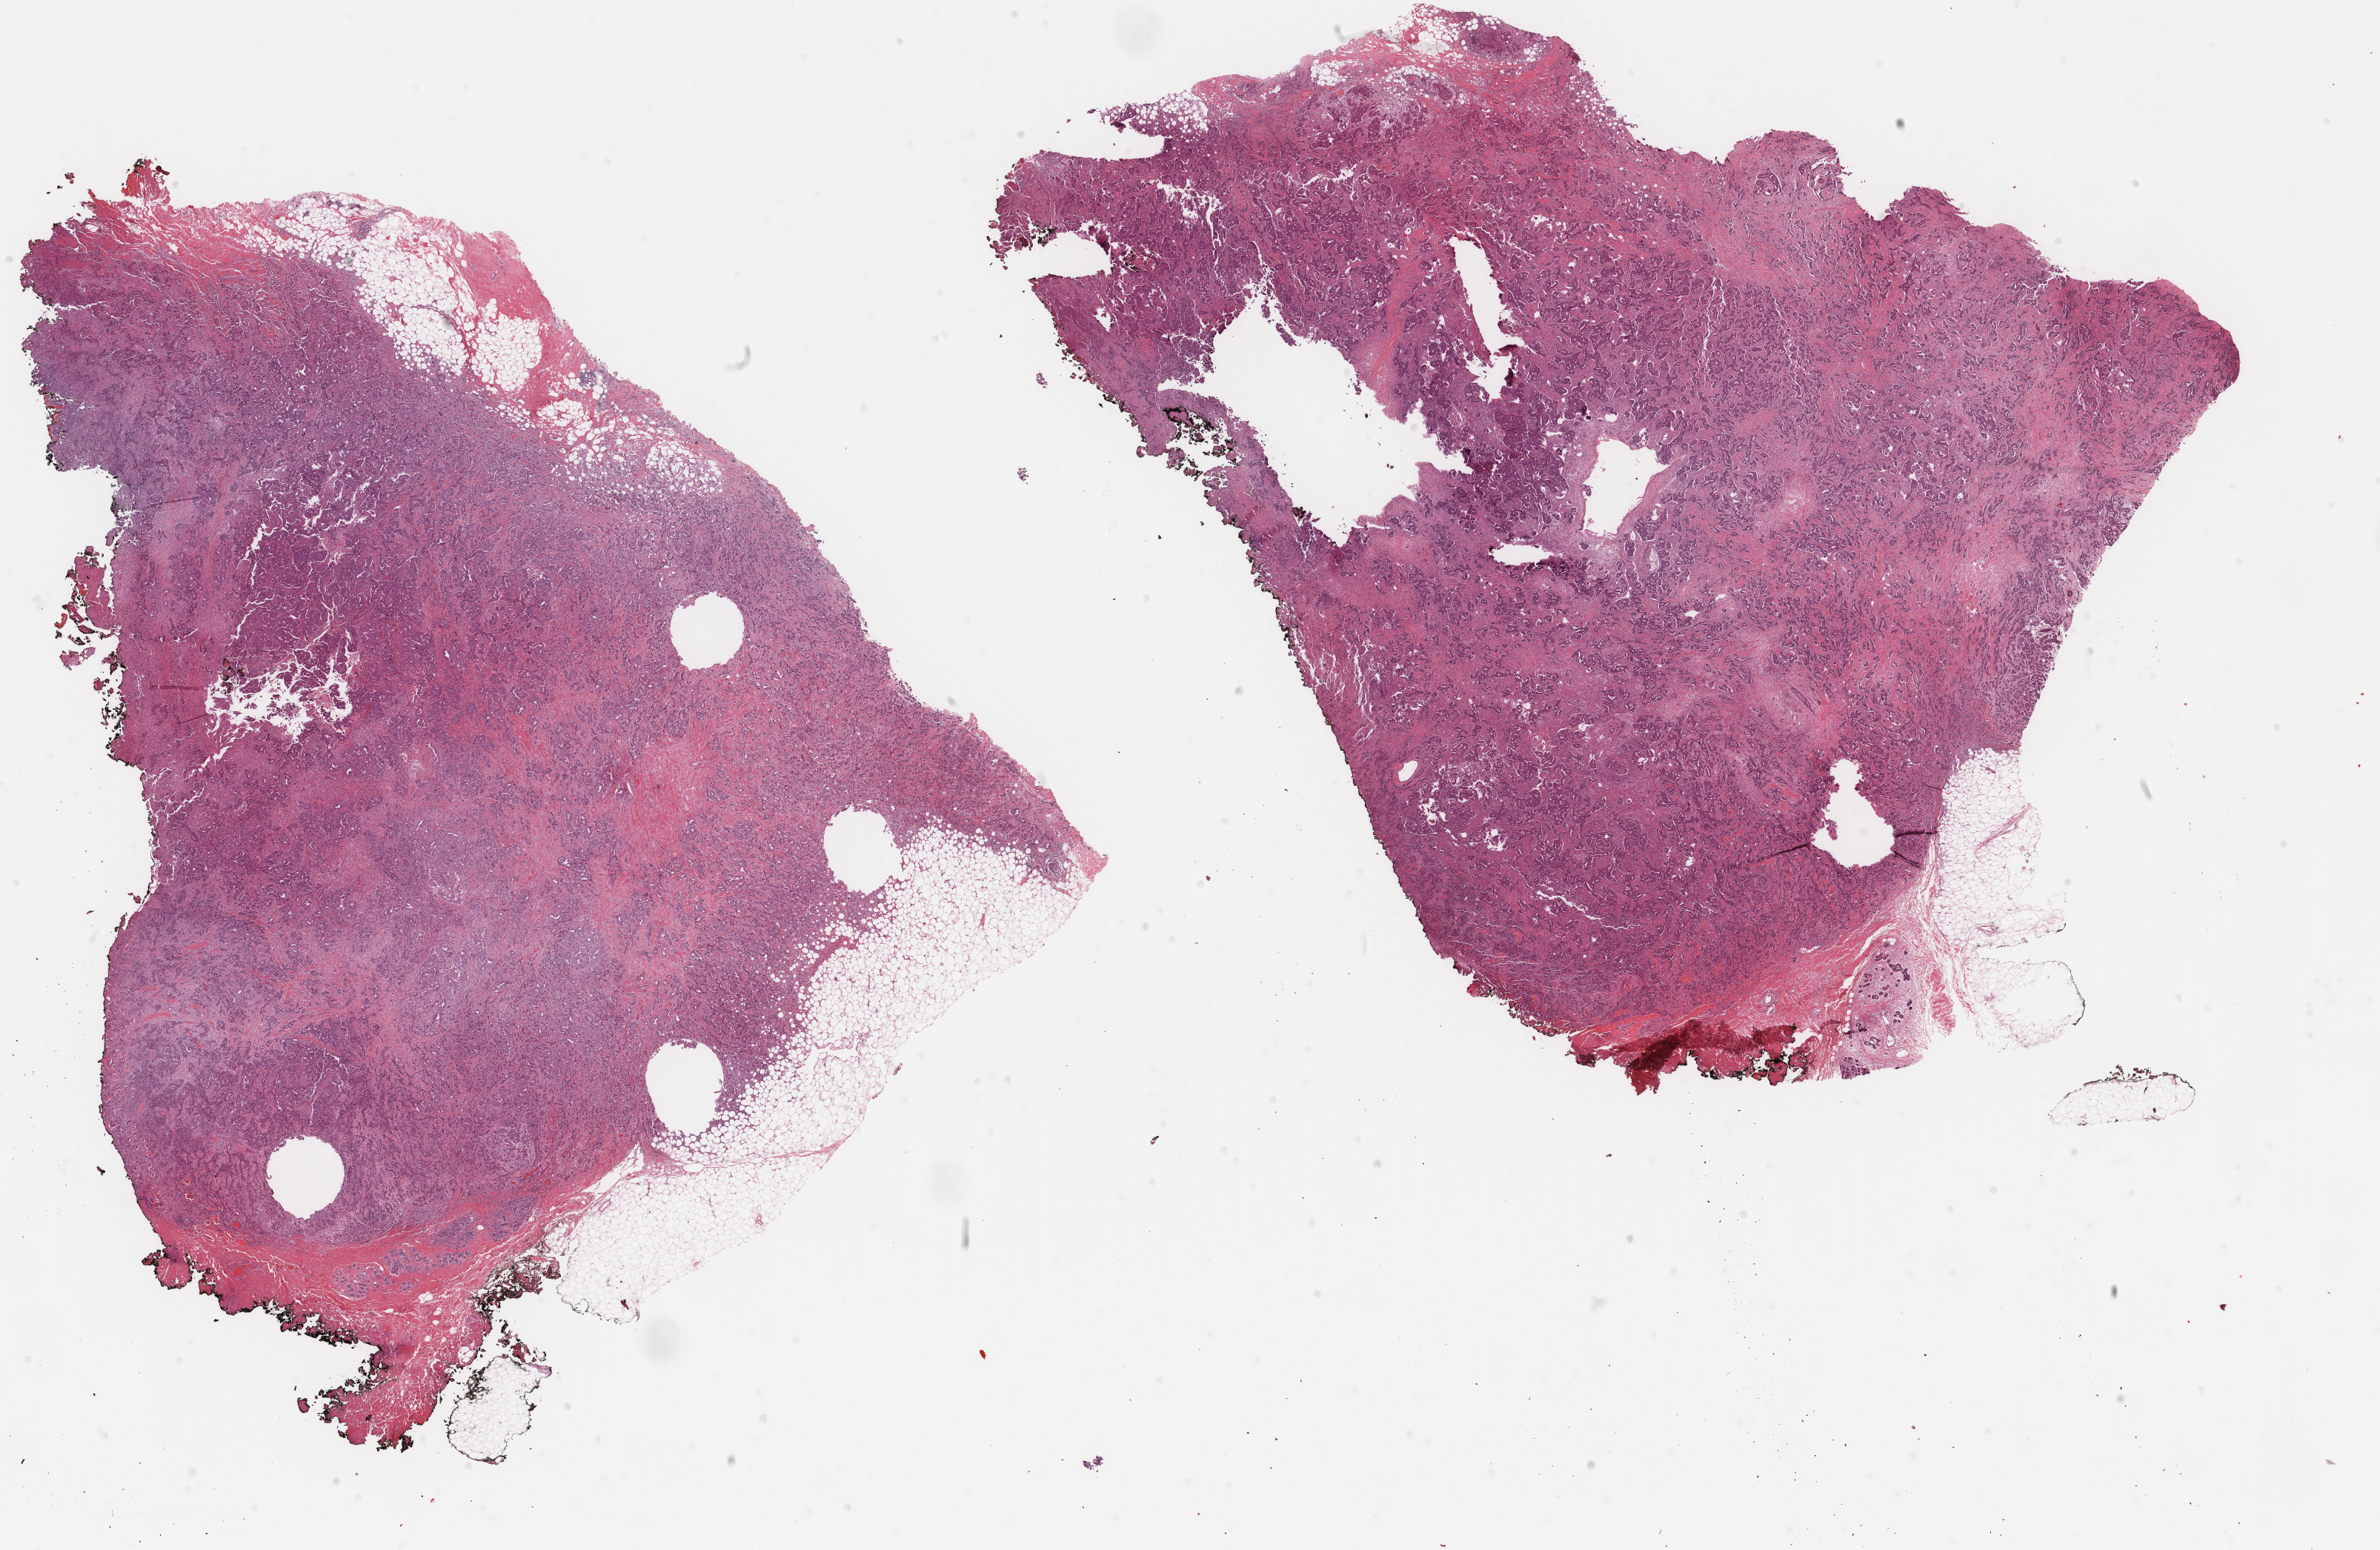
Whole-slide histology image, H&E-stained — a low-resolution overview of the entire scanned area, about 25.5 x 16.6 mm (slide scanned at 40x), formalin-fixed paraffin-embedded (FFPE) diagnostic section, sample: primary tumour, breast. Patient: female, age at initial diagnosis 50 years.
Histologic diagnosis: Infiltrating duct carcinoma, NOS.